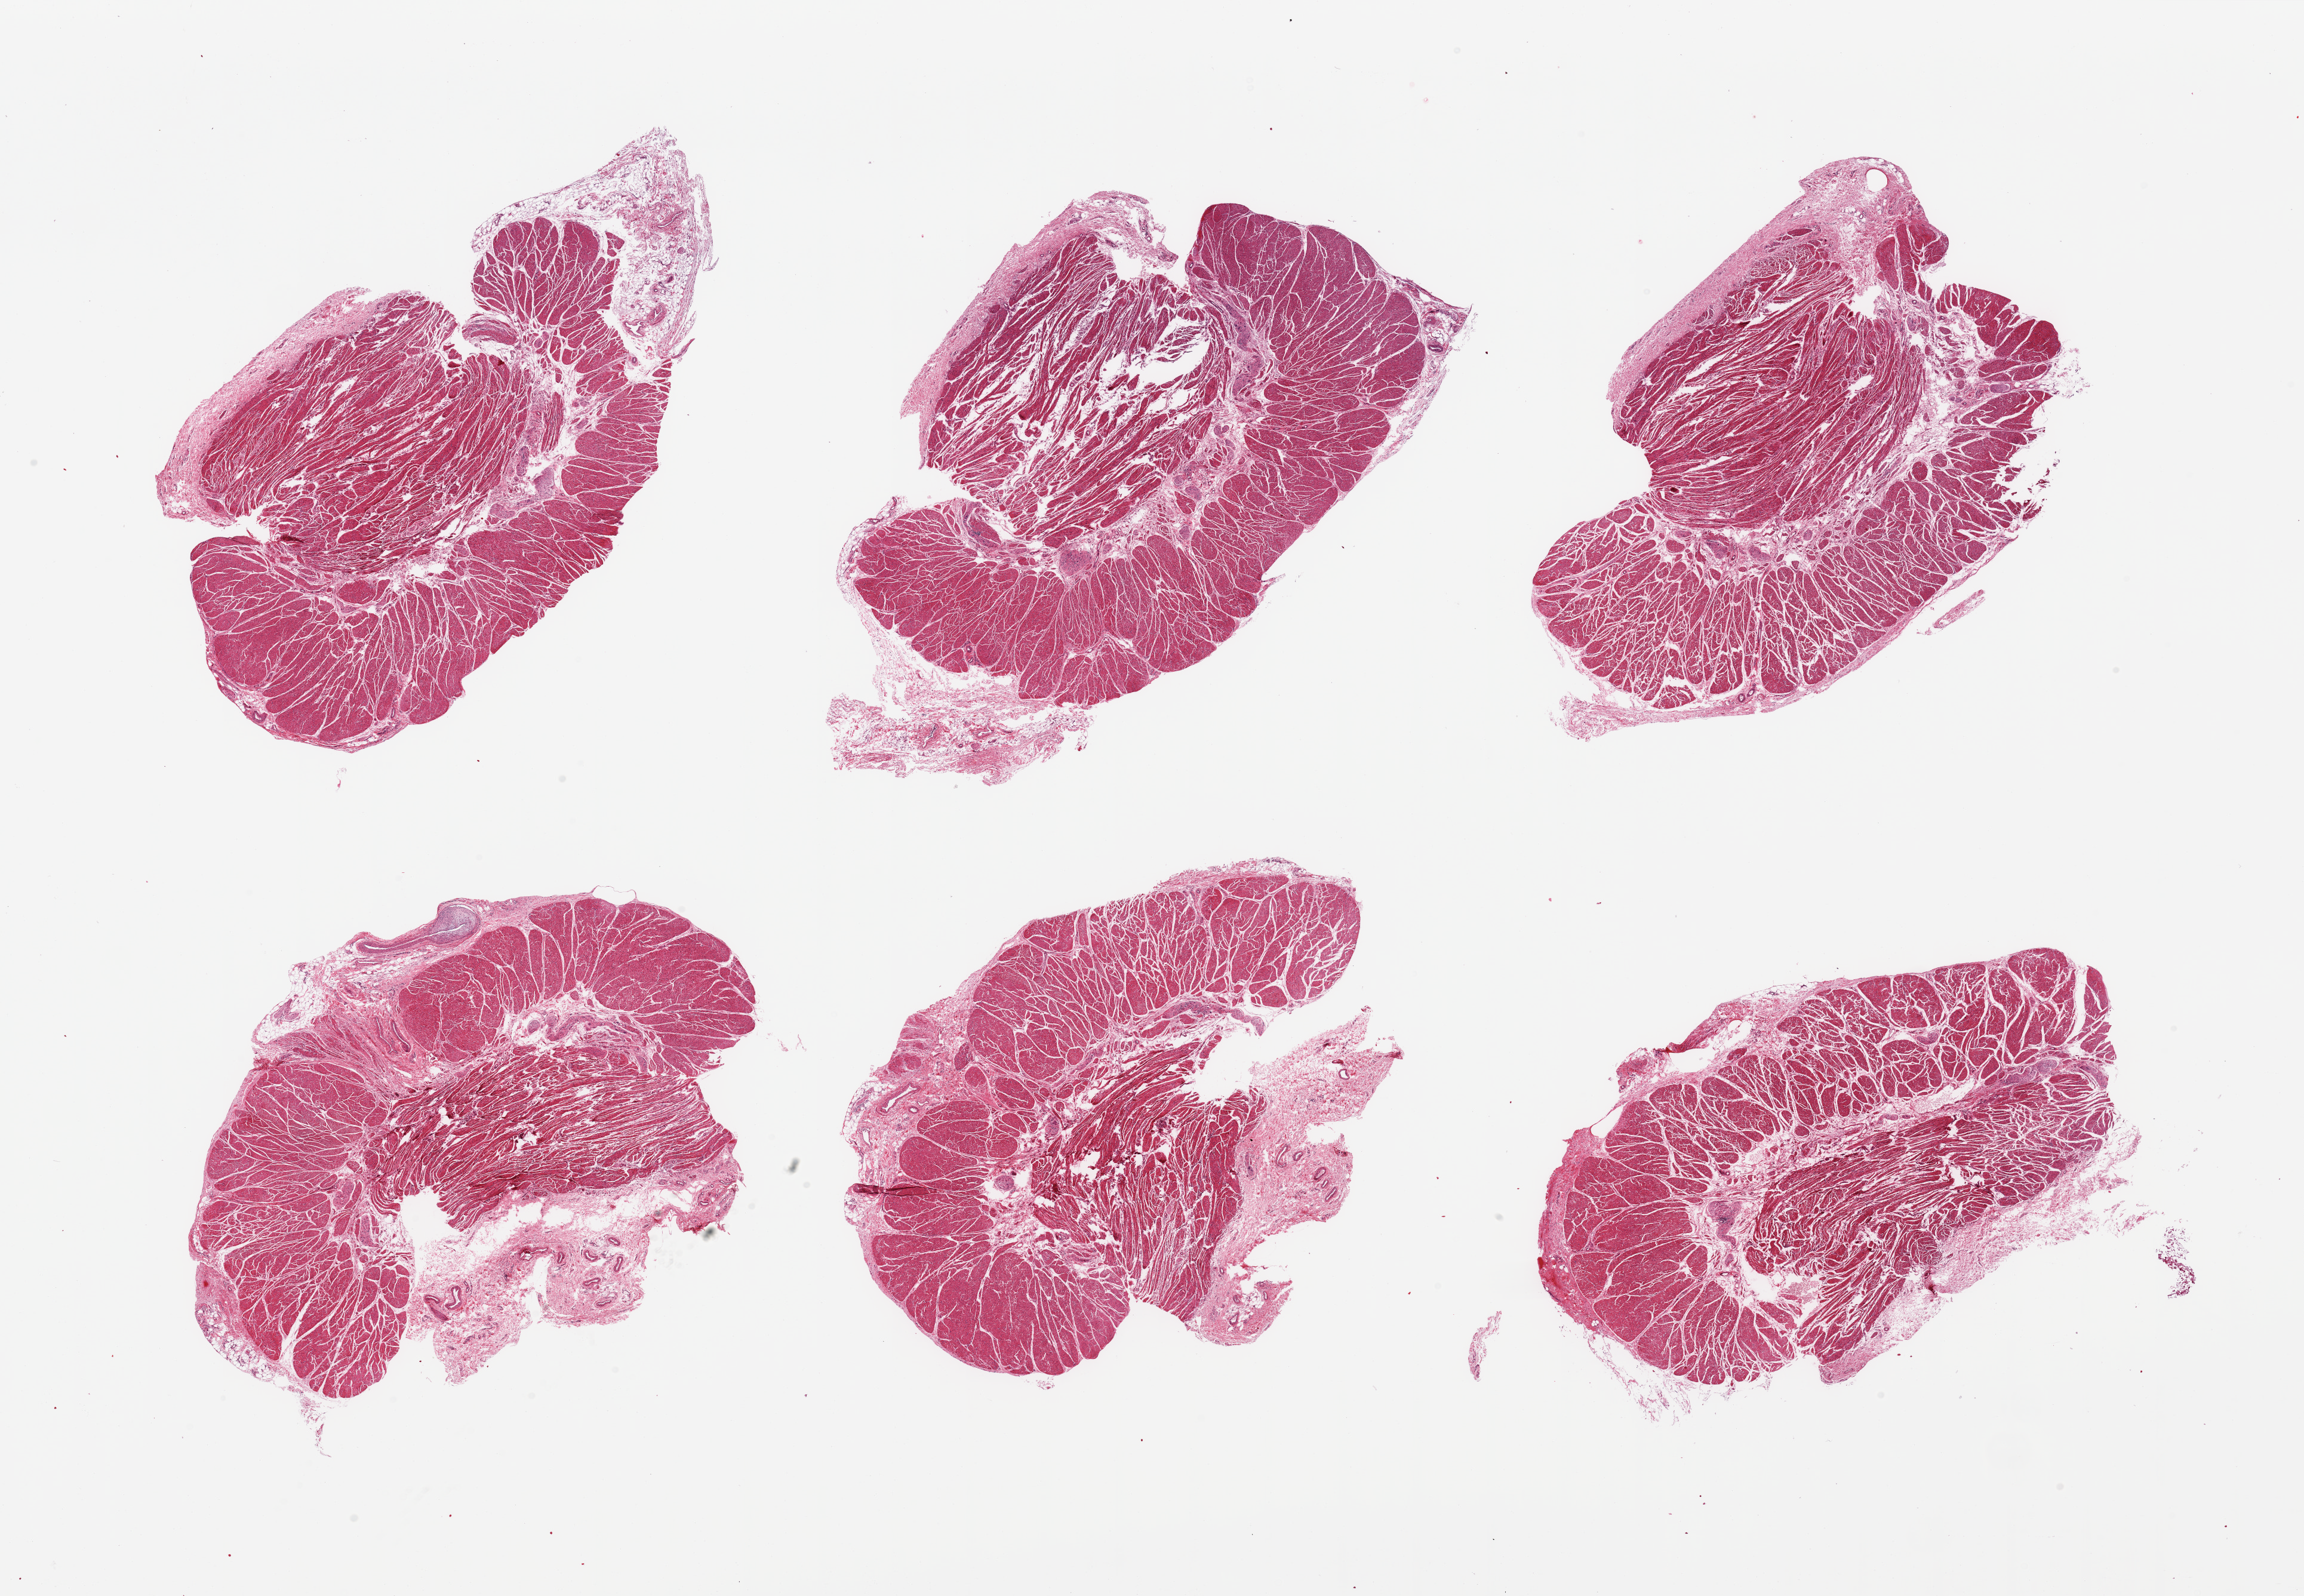
Digitized haematoxylin and eosin-stained section, low-resolution overview of the scanned area, about 30.5 x 21.1 mm, PAXgene-fixed paraffin-embedded (PFPE) section, target tissue: esophageal muscle, donor tissue sample. Male donor.
Review note (as recorded): 6 pieces; 5-20% stromal content.